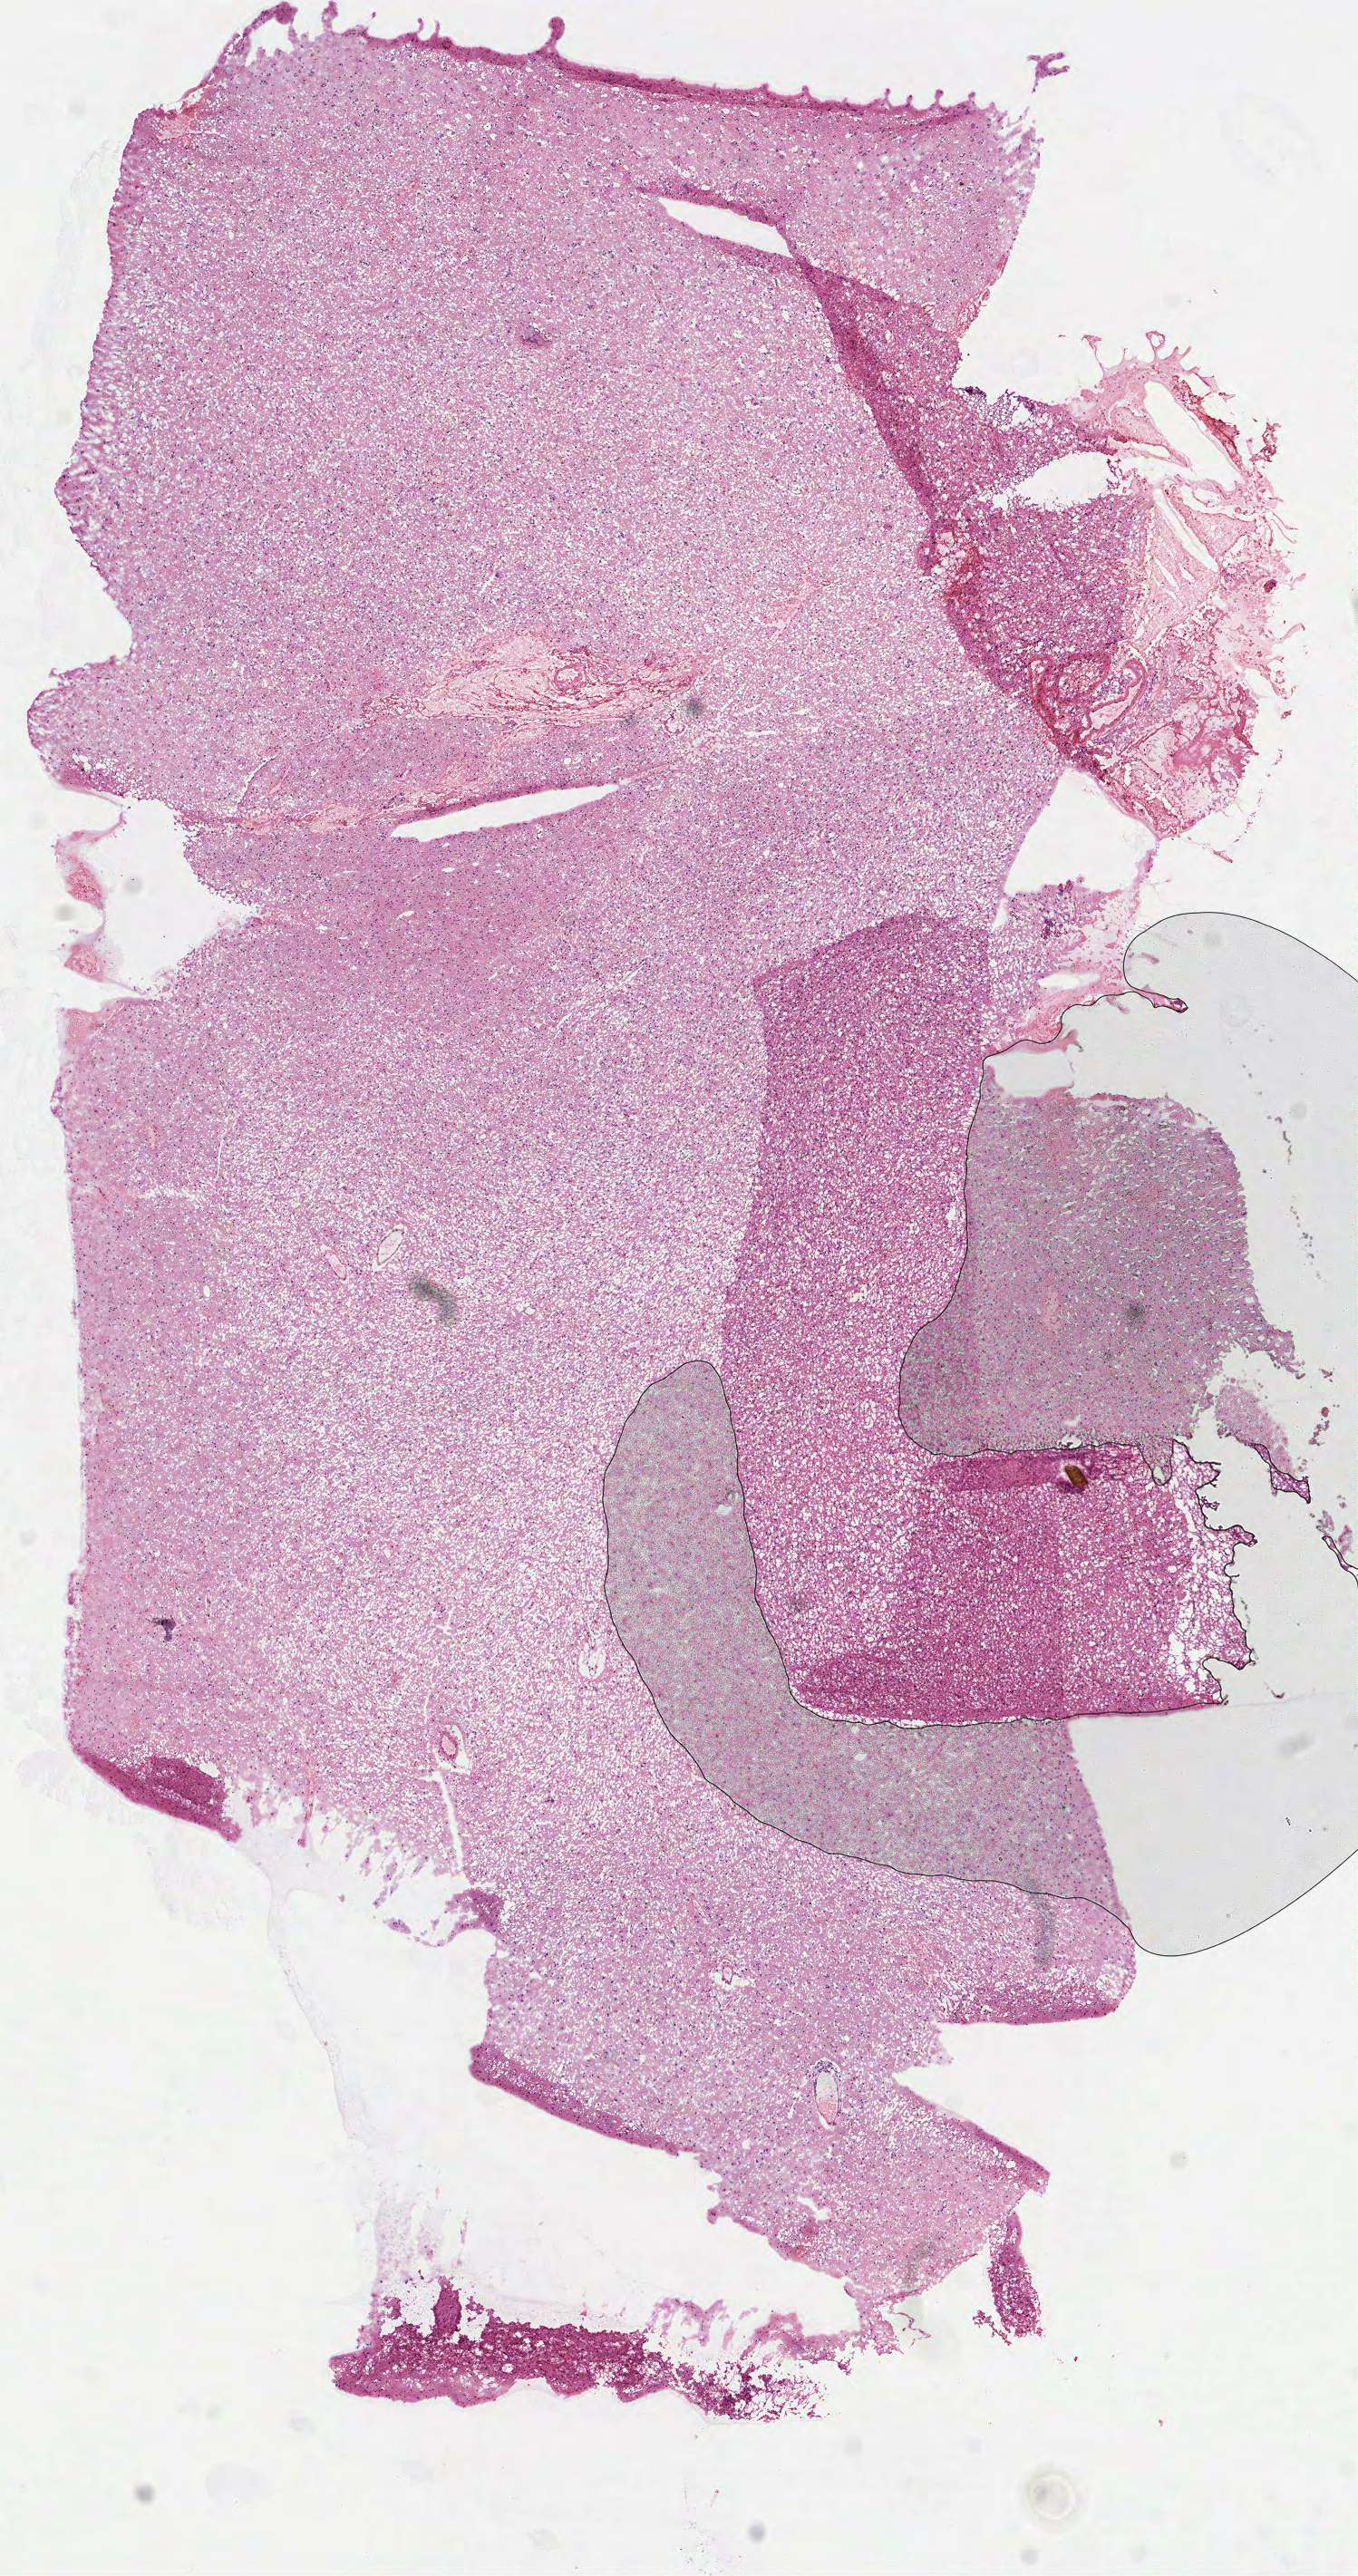
Digitized Hematoxylin and eosin (H&E) stained tissue section (whole slide) — shown as a low-resolution overview of the whole scanned area (about 6.0 x 11.5 mm). Frozen section from the top of the tissue portion. Sample: primary tumour, brain. Male patient; age at initial diagnosis 39 years. Histologic grade: G2 (moderately differentiated). Pathologist review of this section (percent, as recorded): tumour cells 100%, tumour nuclei 70%, normal cells 0%, stromal cells 0%, necrosis 0%.
Pathologic diagnosis: Oligodendroglioma, NOS.